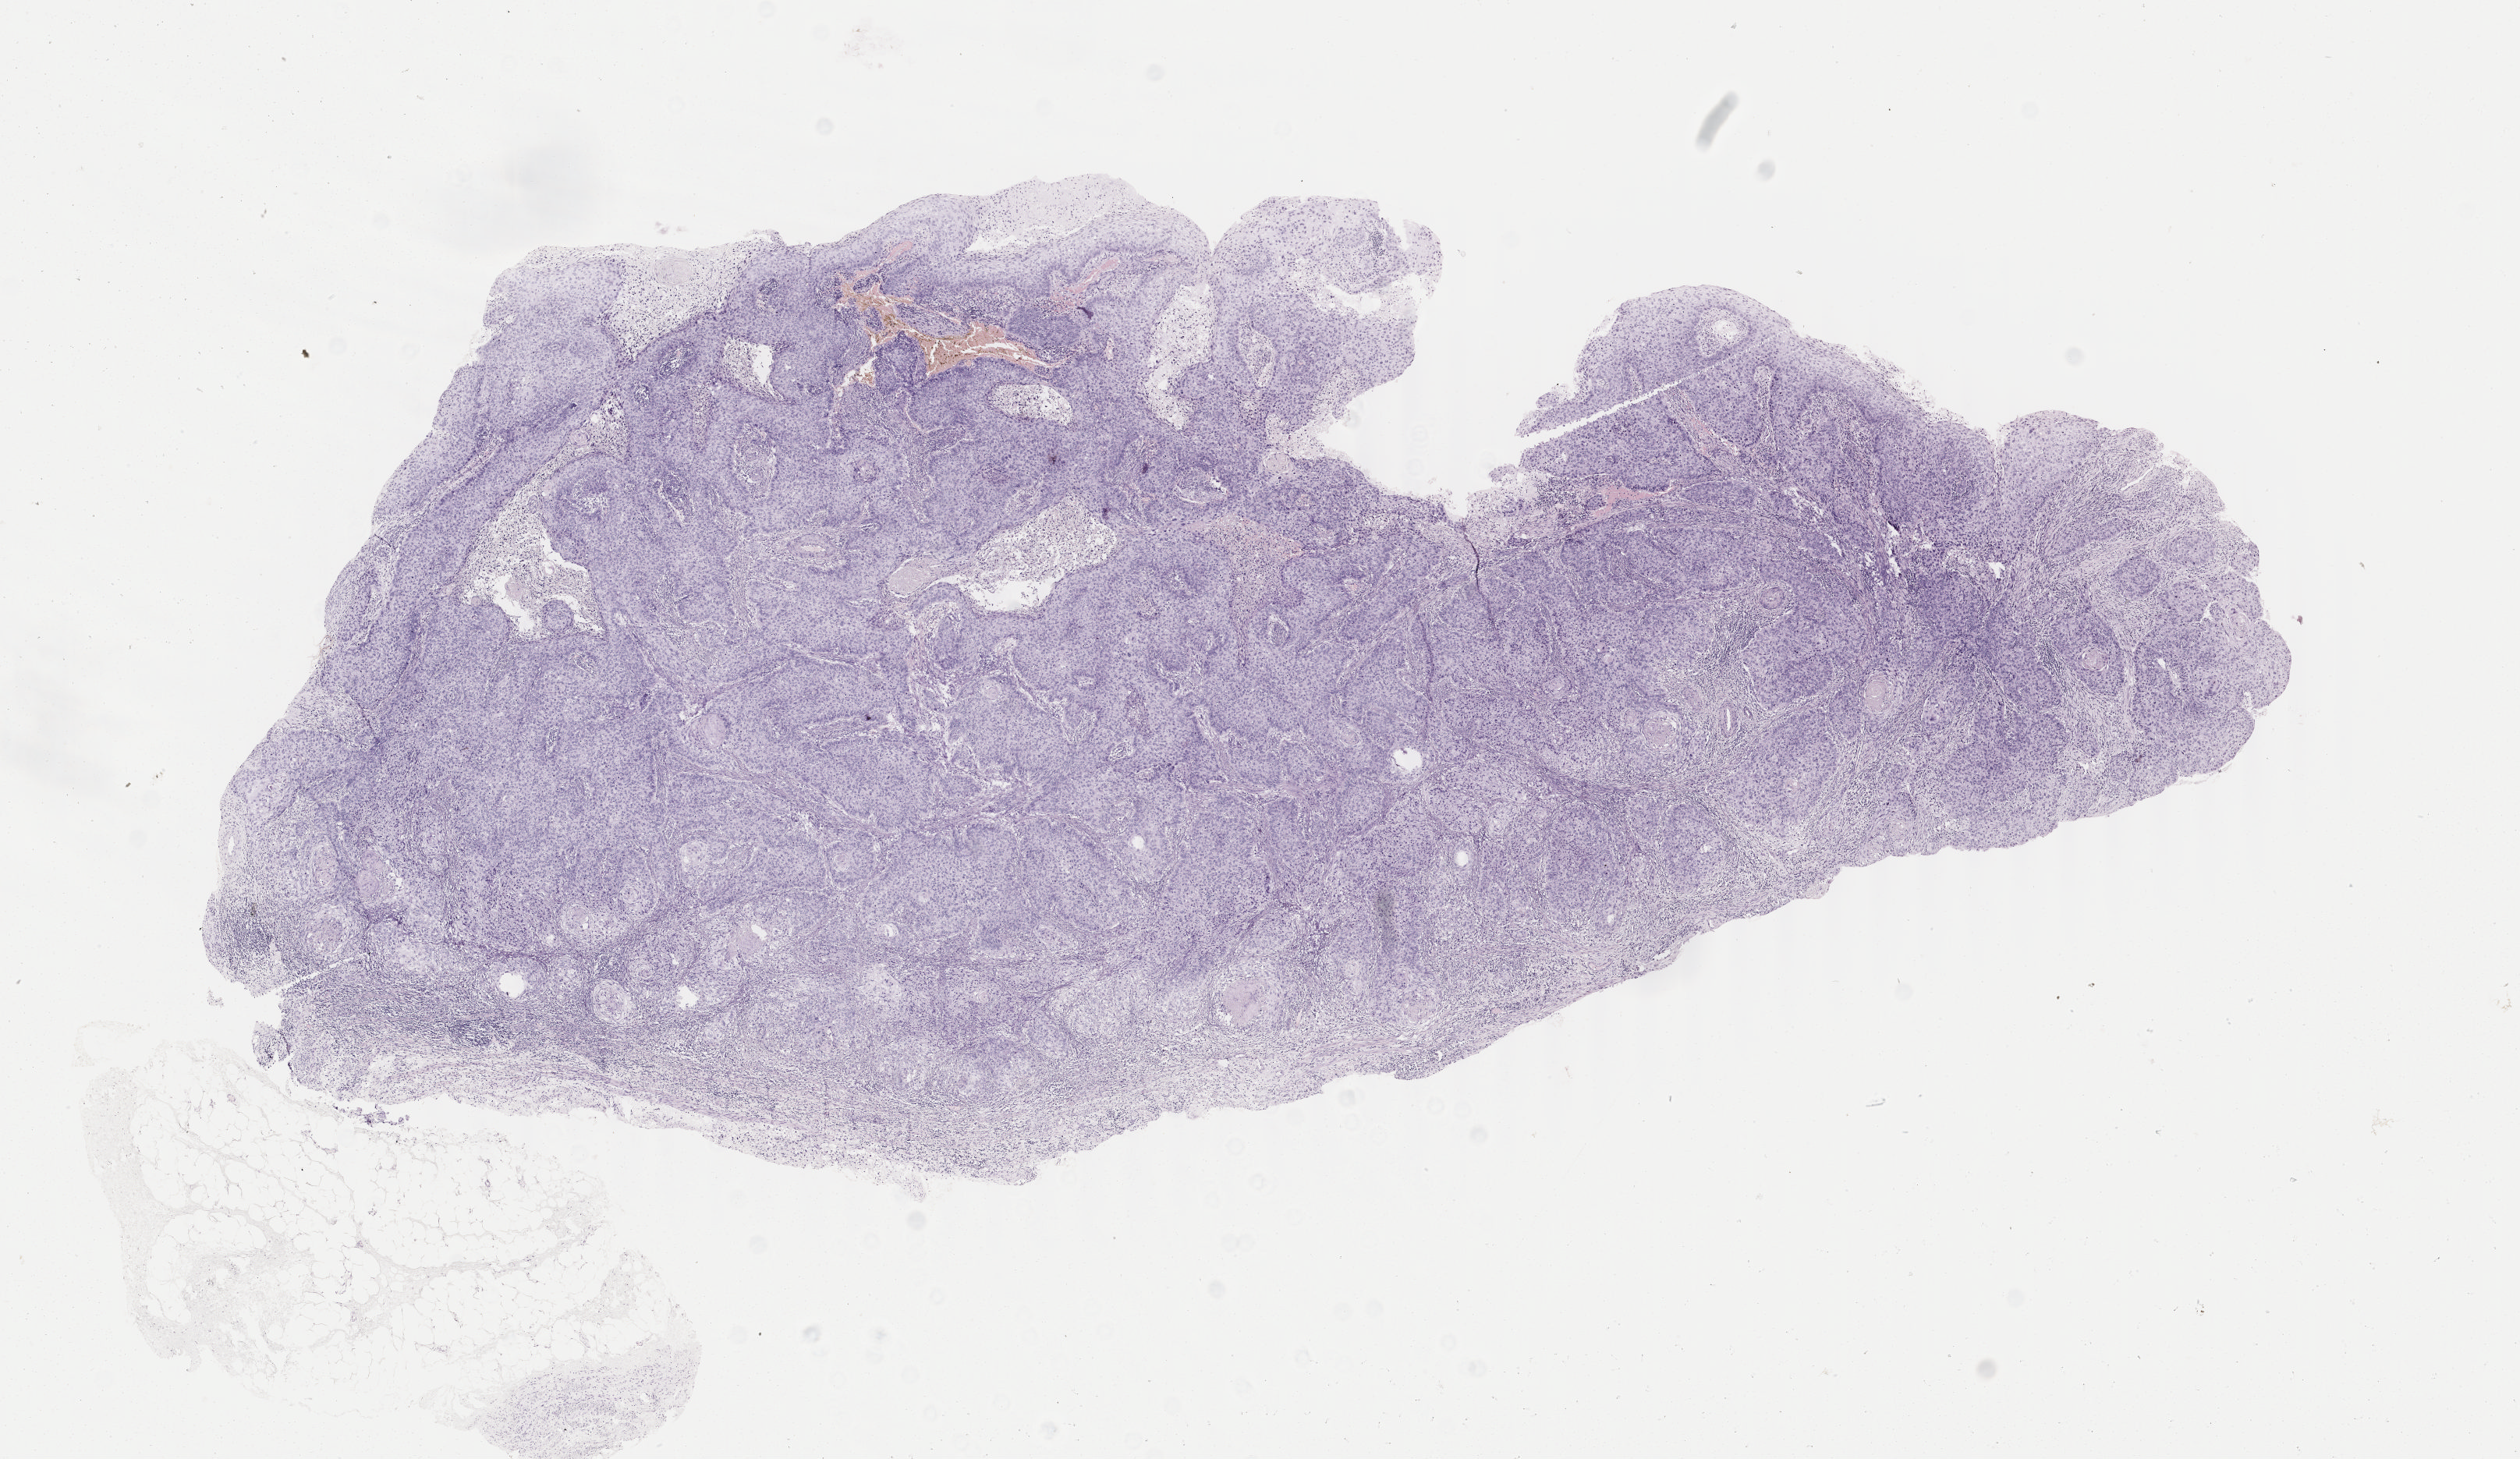
Digitized H&E-stained tissue section (whole slide) — shown as a low-resolution overview of the whole scanned area (about 12.8 x 7.4 mm). Formalin-fixed paraffin-embedded (FFPE) diagnostic section. Cervix, primary tumour sample. Female, age 63 years at initial diagnosis. Histologic grade: G2 (moderately differentiated).
FIGO stage: IB. Histologic diagnosis: Squamous cell carcinoma, keratinizing, NOS (cervix uteri).